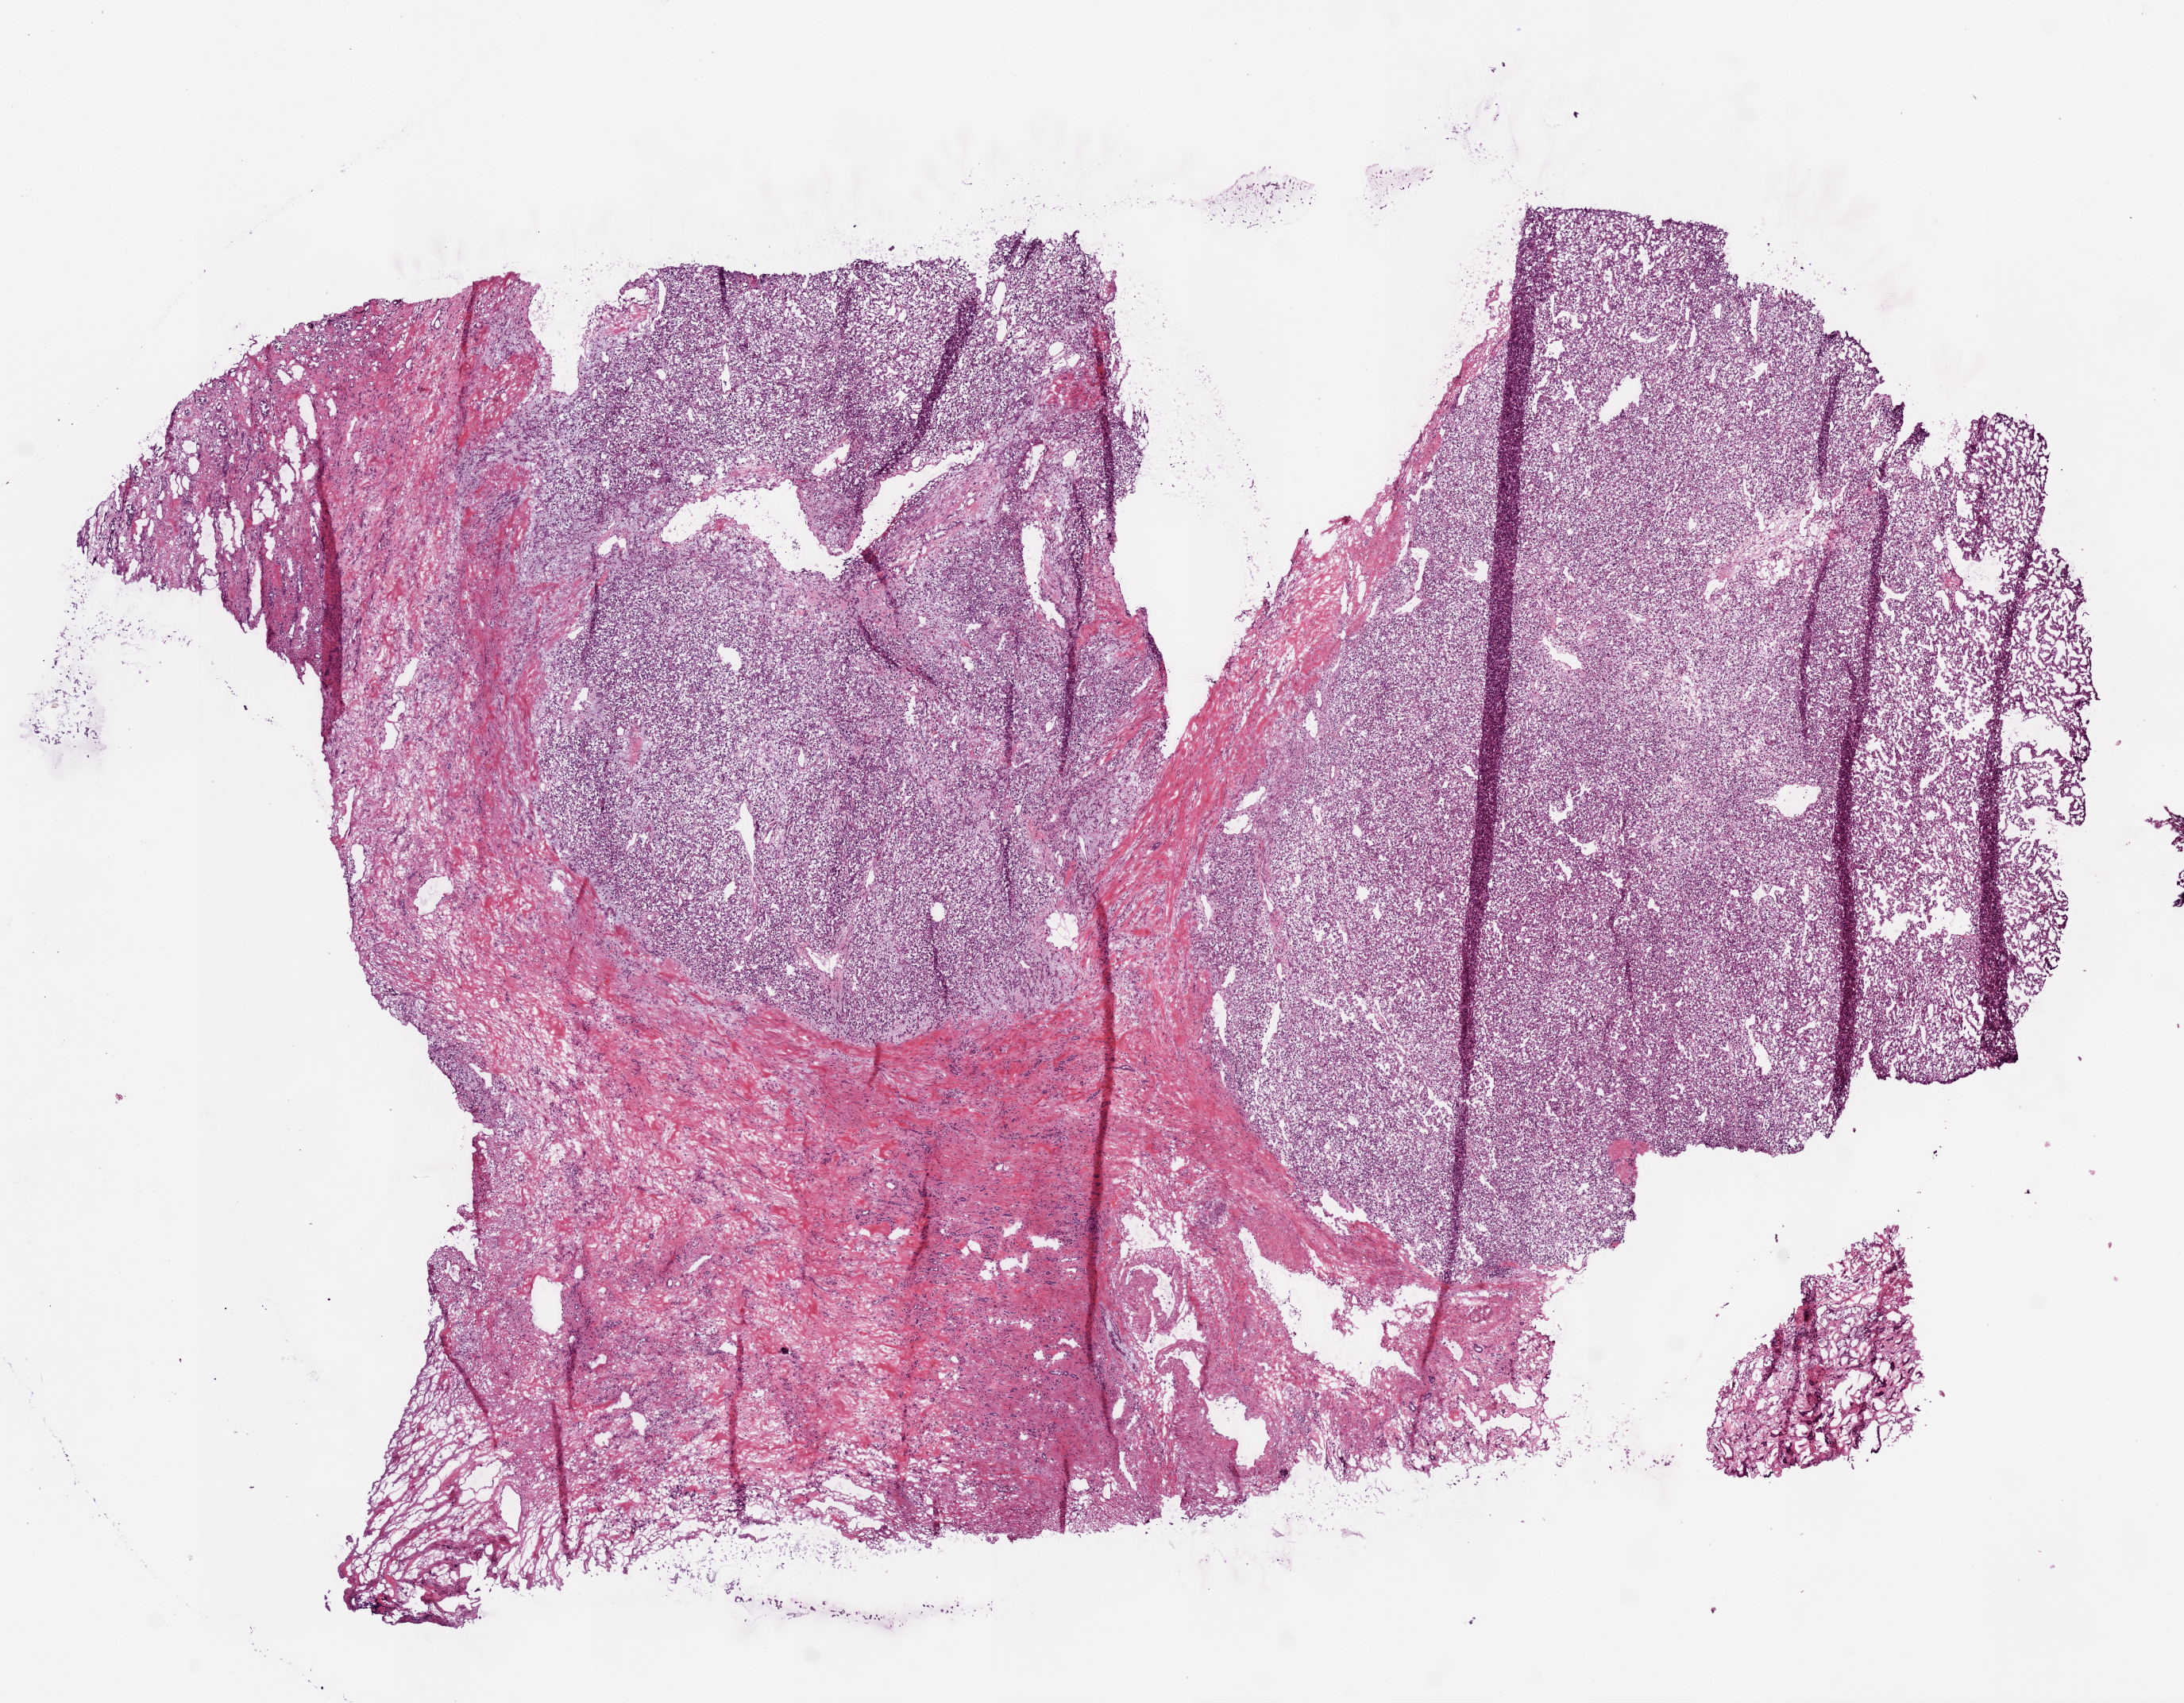
Whole-slide histology image, H&E, low-resolution overview of the scanned area, about 11.0 x 8.6 mm (acquisition: 20x scan). Frozen section from the bottom of the tissue portion. Primary tumour sample from the kidney. Male, age 58 years at initial diagnosis. Histologic grade: G3 (poorly differentiated). Slide review estimates, as recorded: tumour cells 60%, tumour nuclei 80%, normal cells 5%, stromal cells 35%, necrosis 0%.
Pathologic diagnosis: Clear cell adenocarcinoma, NOS. AJCC pathologic stage: III.